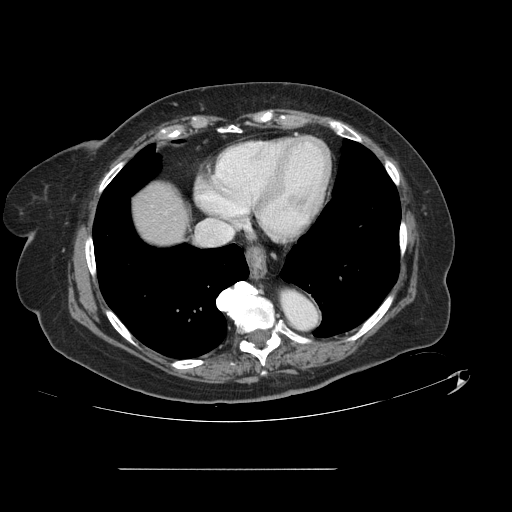
Contrast-enhanced abdominal CT, one axial slice. Slice 128 of 148 in the series (ordered by position). 120 kVp. Intravenous contrast given. Soft-tissue window (W 400 / L 40 HU). 512 × 512 image matrix. Female patient, age 75 years. Case-level facts recorded for this patient, not image findings: diagnosis: colorectal cancer liver metastases, imaged before liver resection; multiple liver metastases: no; largest metastasis: 2.4 cm.
Outlined on this slice (outlined manually by an expert reader):
- liver: box from (x=134, y=183) to (x=185, y=243) px
- planned liver remnant (the part of the liver to remain after resection): (x=134, y=183)–(x=185, y=244)